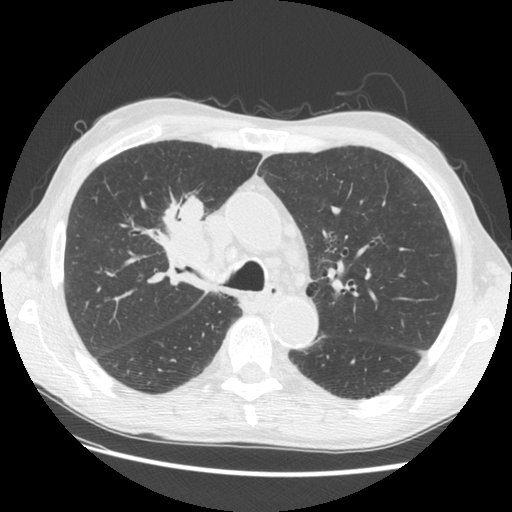
Low-dose screening chest CT, one axial slice; slice 90 of 133 in the series (ordered by position); reconstruction kernel STANDARD; 120 kVp; lung window (W 1500 / L -600 HU); 2.5 mm slice thickness; 512 × 512 image matrix, field of view 360 × 360 mm.
Annotated regions visible in this slice (manually delineated by an expert):
- lesion 1 (tumor, hilum of right lung): box from (x=162, y=194) to (x=208, y=262) px